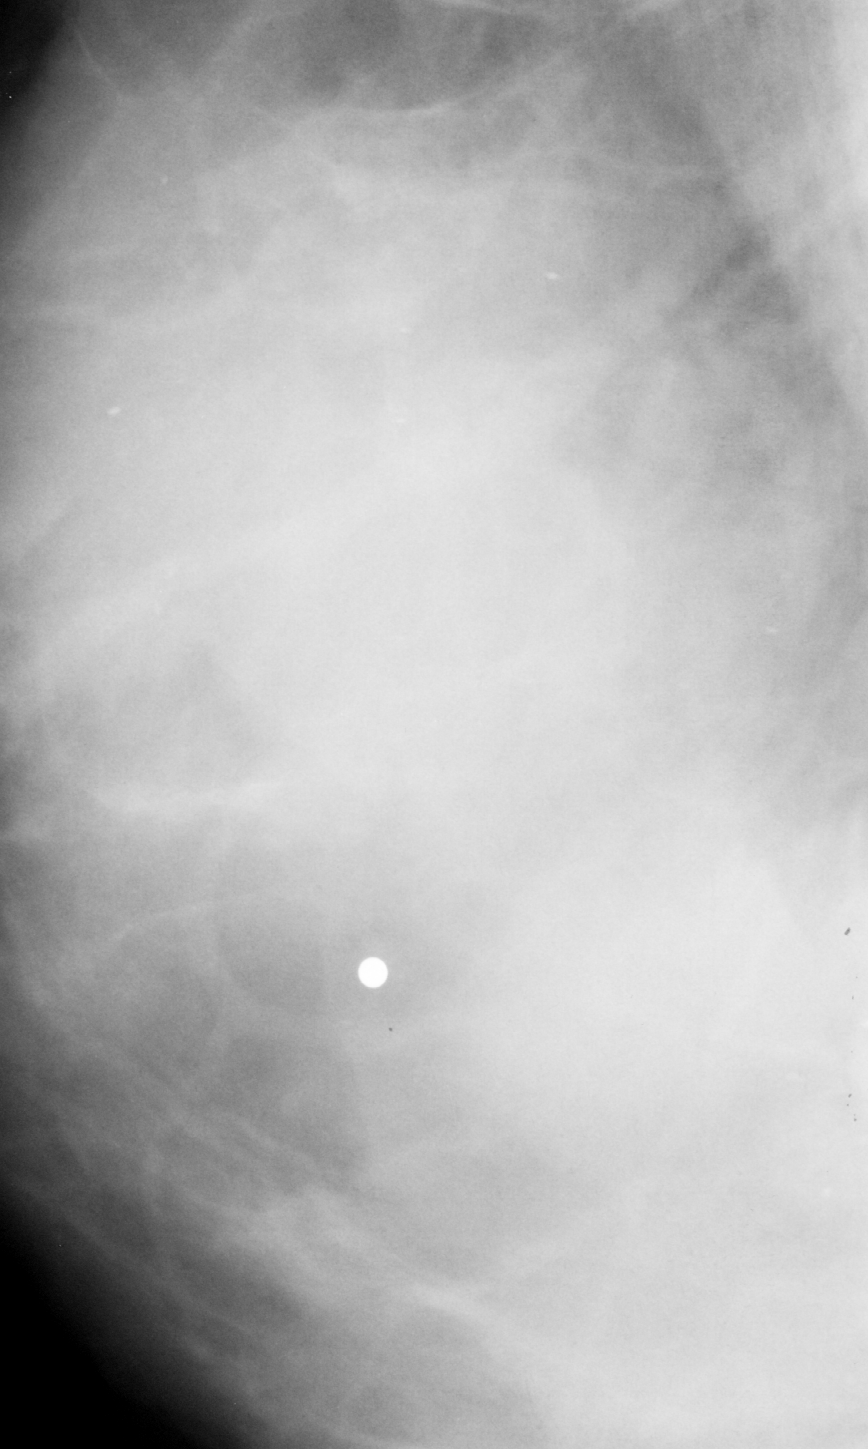
Crop from a digitized film mammogram around one marked abnormality, right breast, MLO view, BI-RADS breast density category 4 (scale 1–4).
- Calcifications, morphology punctate, distribution diffusely scattered; BI-RADS assessment category 2; pathology (as recorded): benign.